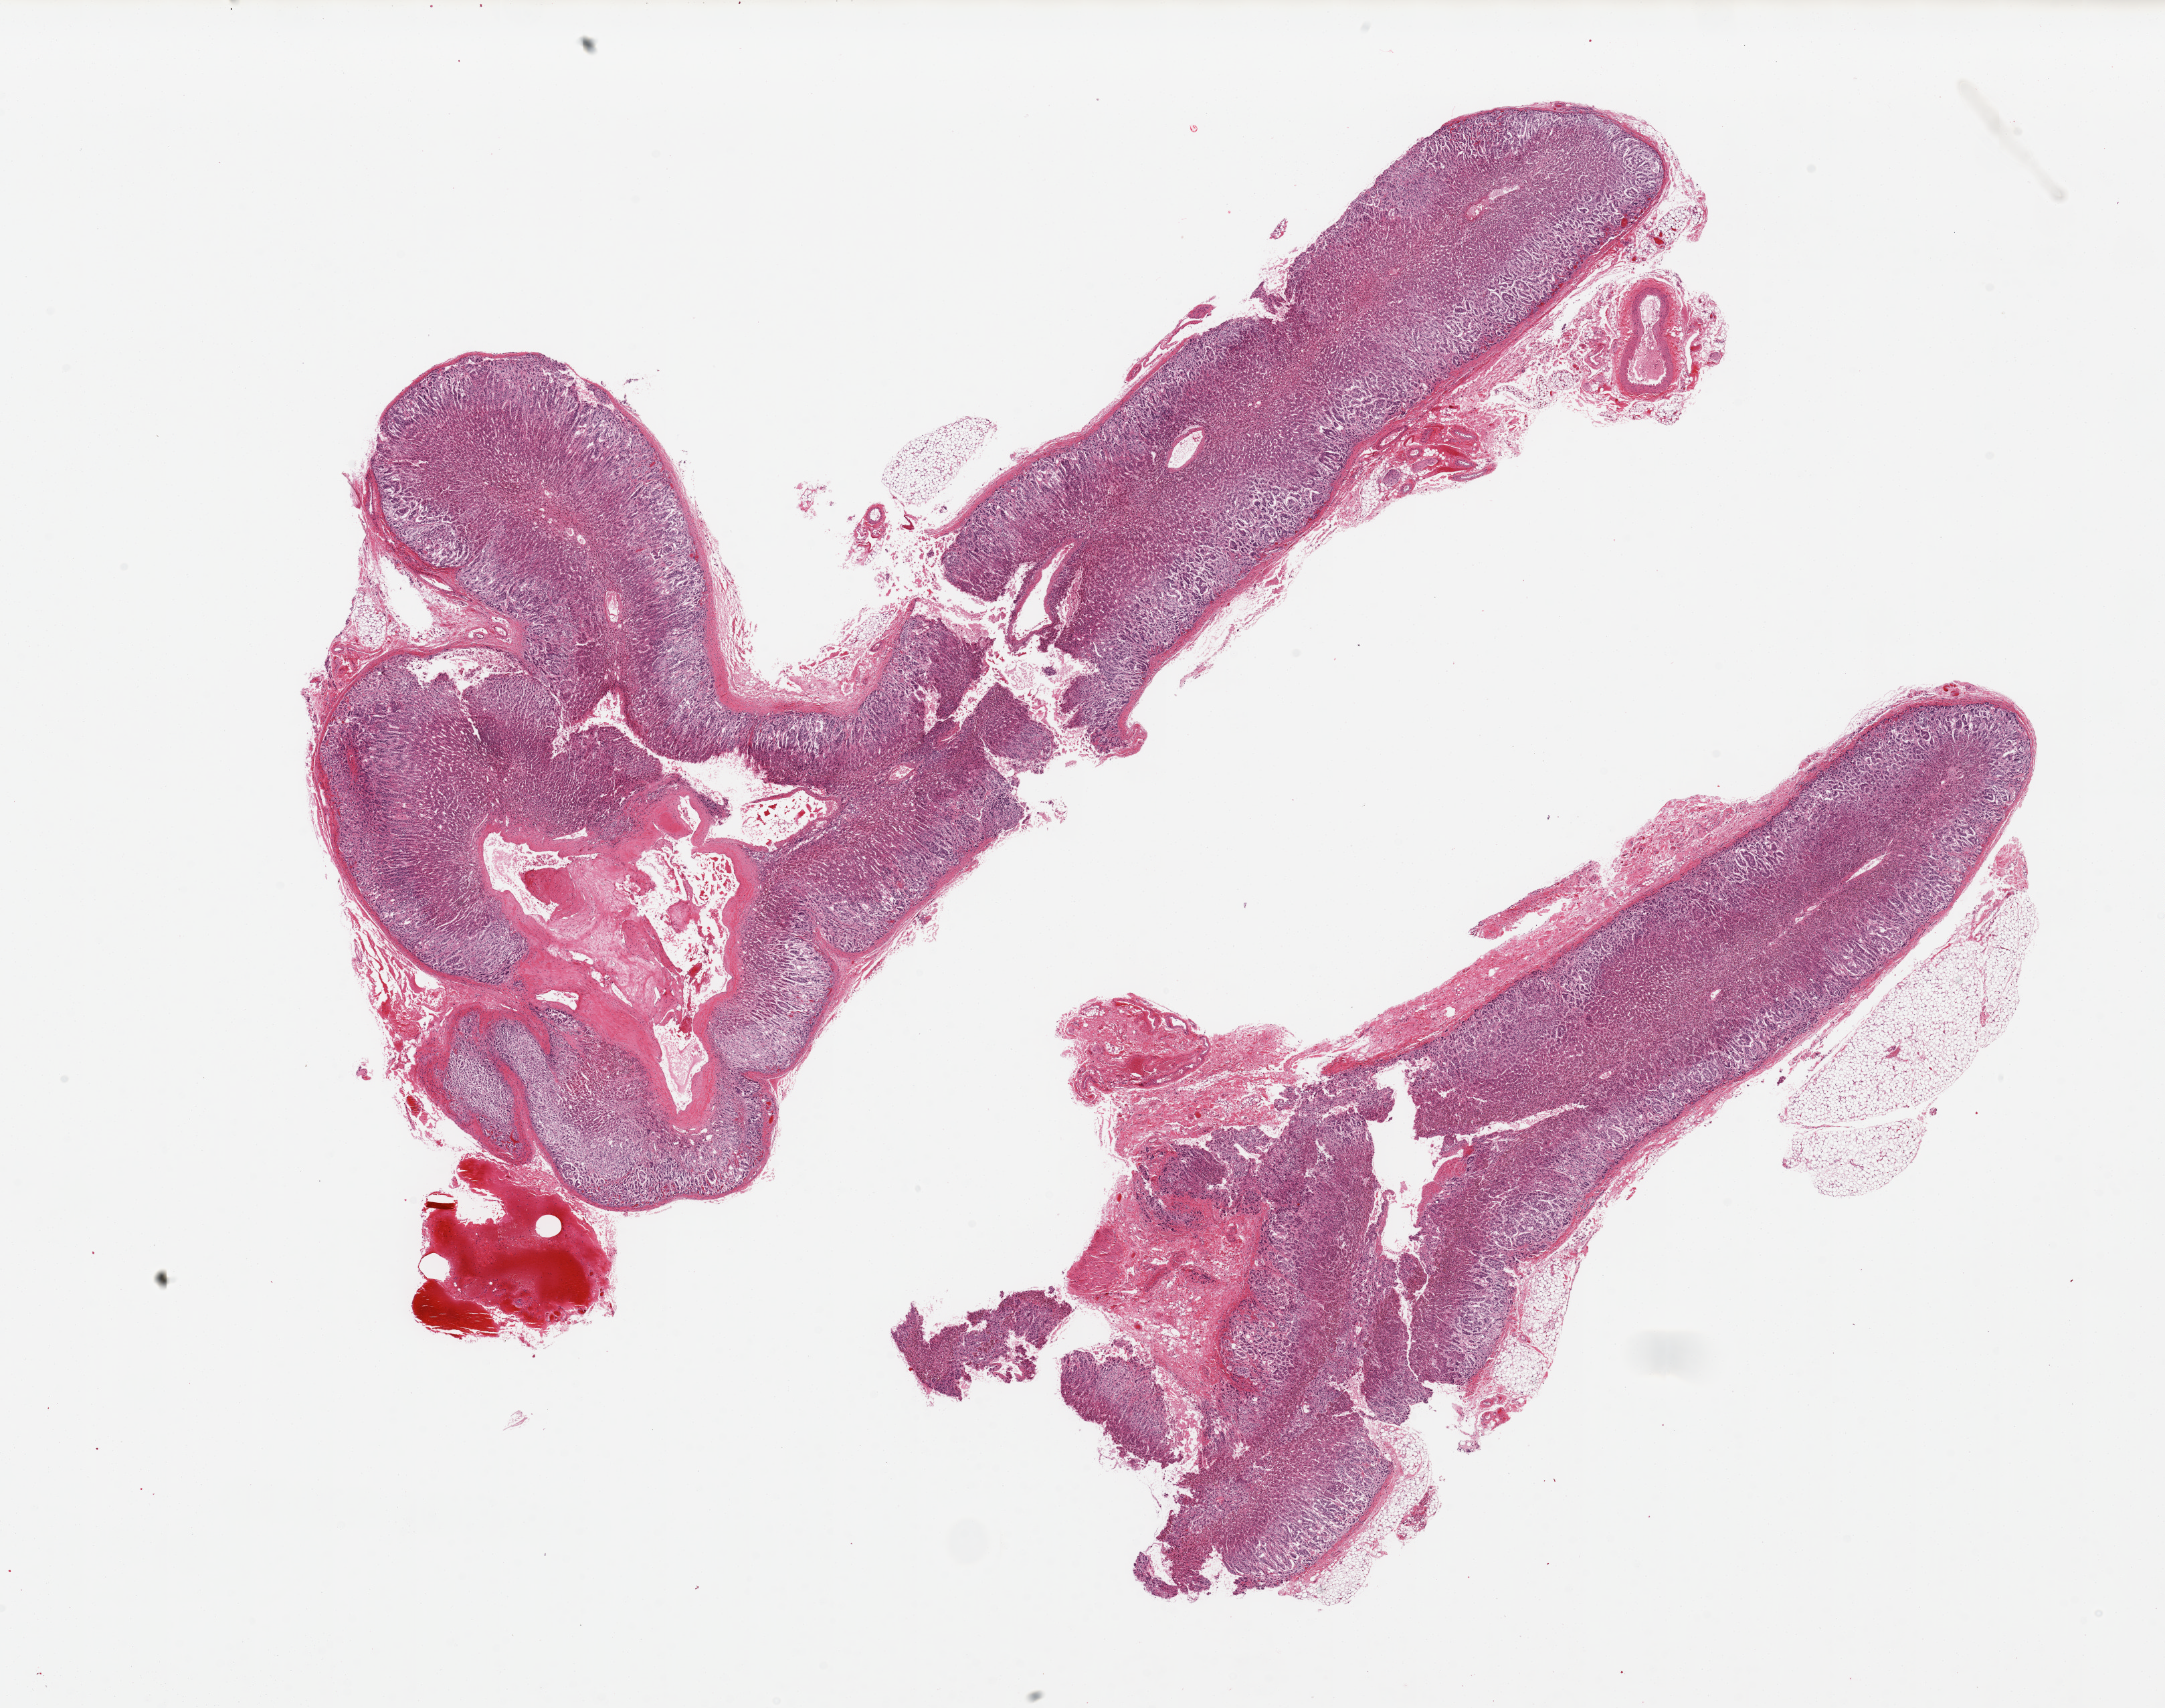
Whole-slide image, haematoxylin and eosin stain, brightfield, shown as a low-resolution overview of the whole scanned area (about 25.6 x 20.2 mm, slide scanned at 20x), PAXgene-fixed paraffin-embedded (PFPE) section, section of adrenal gland (target tissue), donor tissue sample.
• pathologist's review note for this sample: 2 pieces 18x9 & 14x6 mm